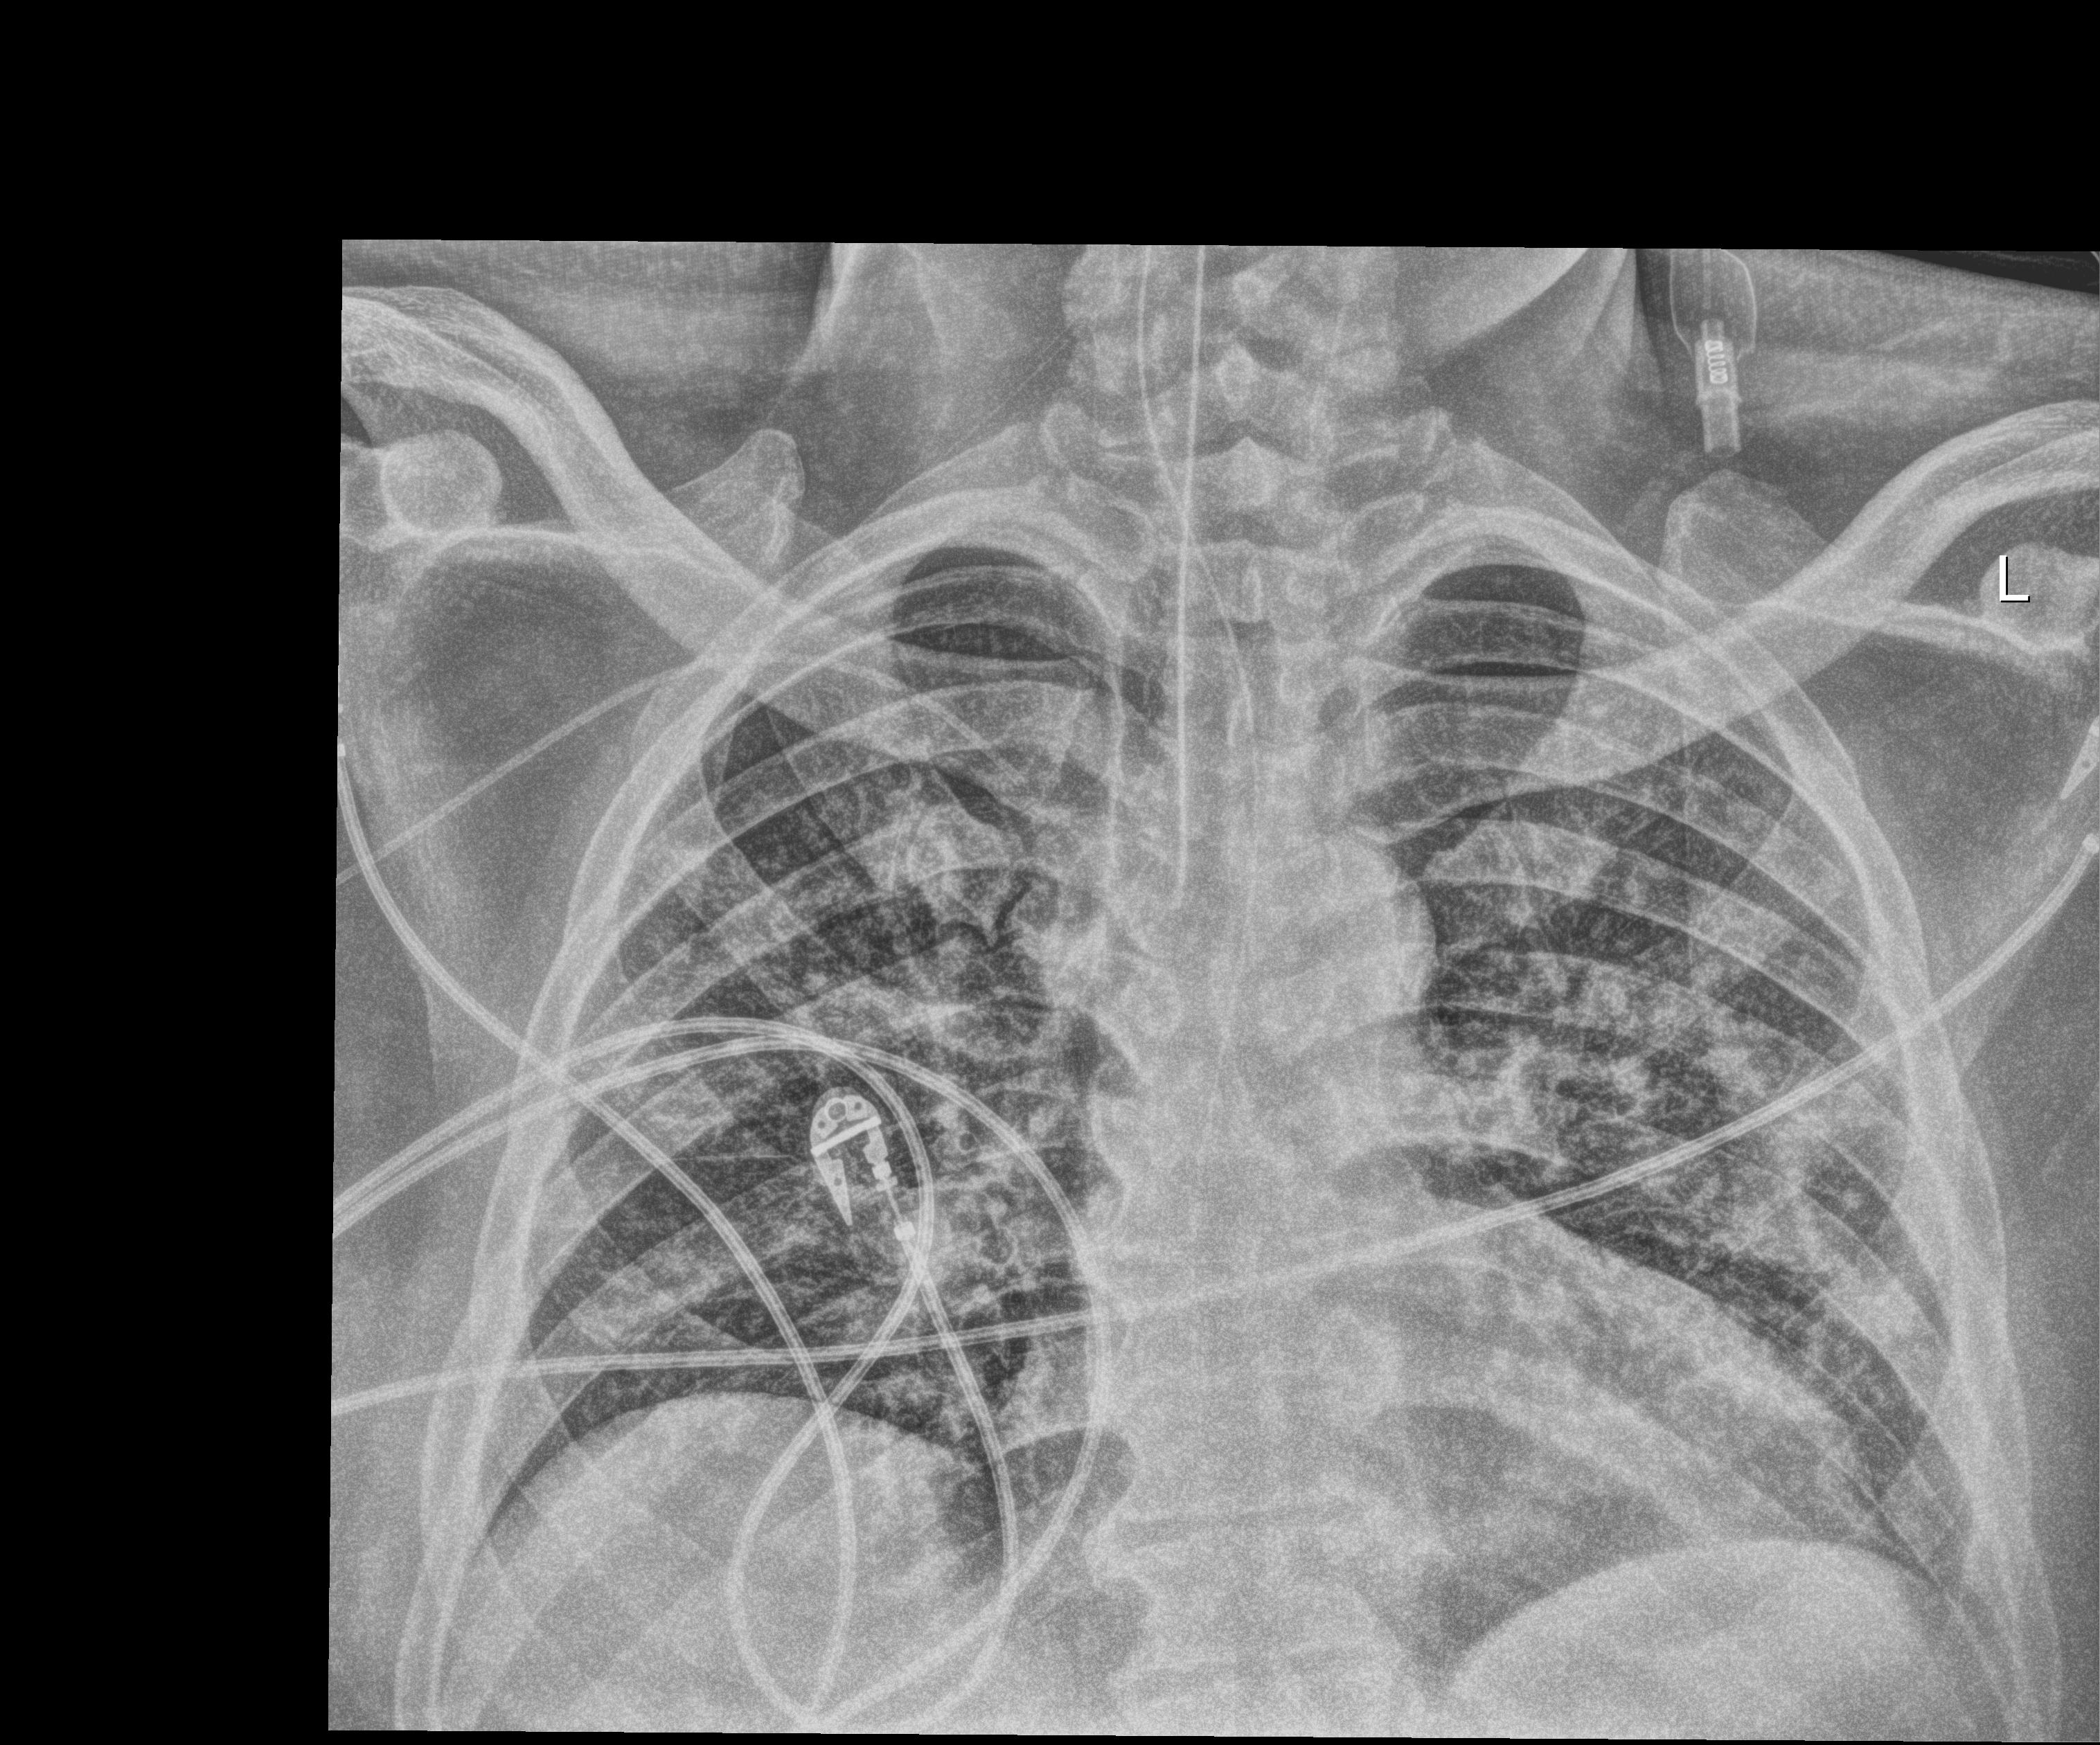
Chest radiograph (digital radiography); anteroposterior (AP) projection. Patient hospitalised with COVID-19; male, aged 18–59 years.
From the hospital-stay record, not from the radiograph (when in the stay this image was taken is not recorded):
- admitted to intensive care during this hospital stay: yes
- mechanically ventilated during this hospital stay: yes